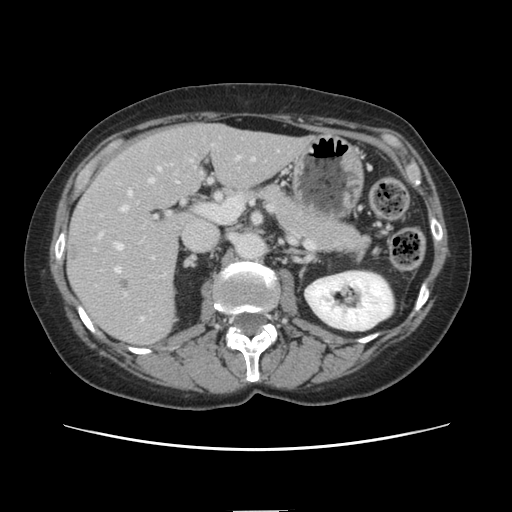
Contrast-enhanced abdominal CT, one axial slice. Position 70 of 141 along the scan axis. Intravenous contrast given. Soft-tissue window (W 400 / L 40 HU). 2.5 mm slice thickness. 512 × 512 image matrix. Female patient, age 63 years. Case-level facts recorded for this patient, not image findings: diagnosis: colorectal cancer liver metastases, imaged before liver resection; multiple liver metastases: yes; largest metastasis: 3.2 cm.
Outlined on this slice (manually delineated by an expert):
- hepatic veins: bounding box [x1, y1, x2, y2] px = [114, 168, 160, 273]
- liver: [69, 125, 307, 345]
- planned liver remnant (the part of the liver to remain after resection): [175, 125, 307, 191]
- portal vein (with intrahepatic branches): [100, 189, 143, 319]
- liver metastasis: [118, 278, 130, 290]
- liver metastasis: [67, 245, 80, 260]